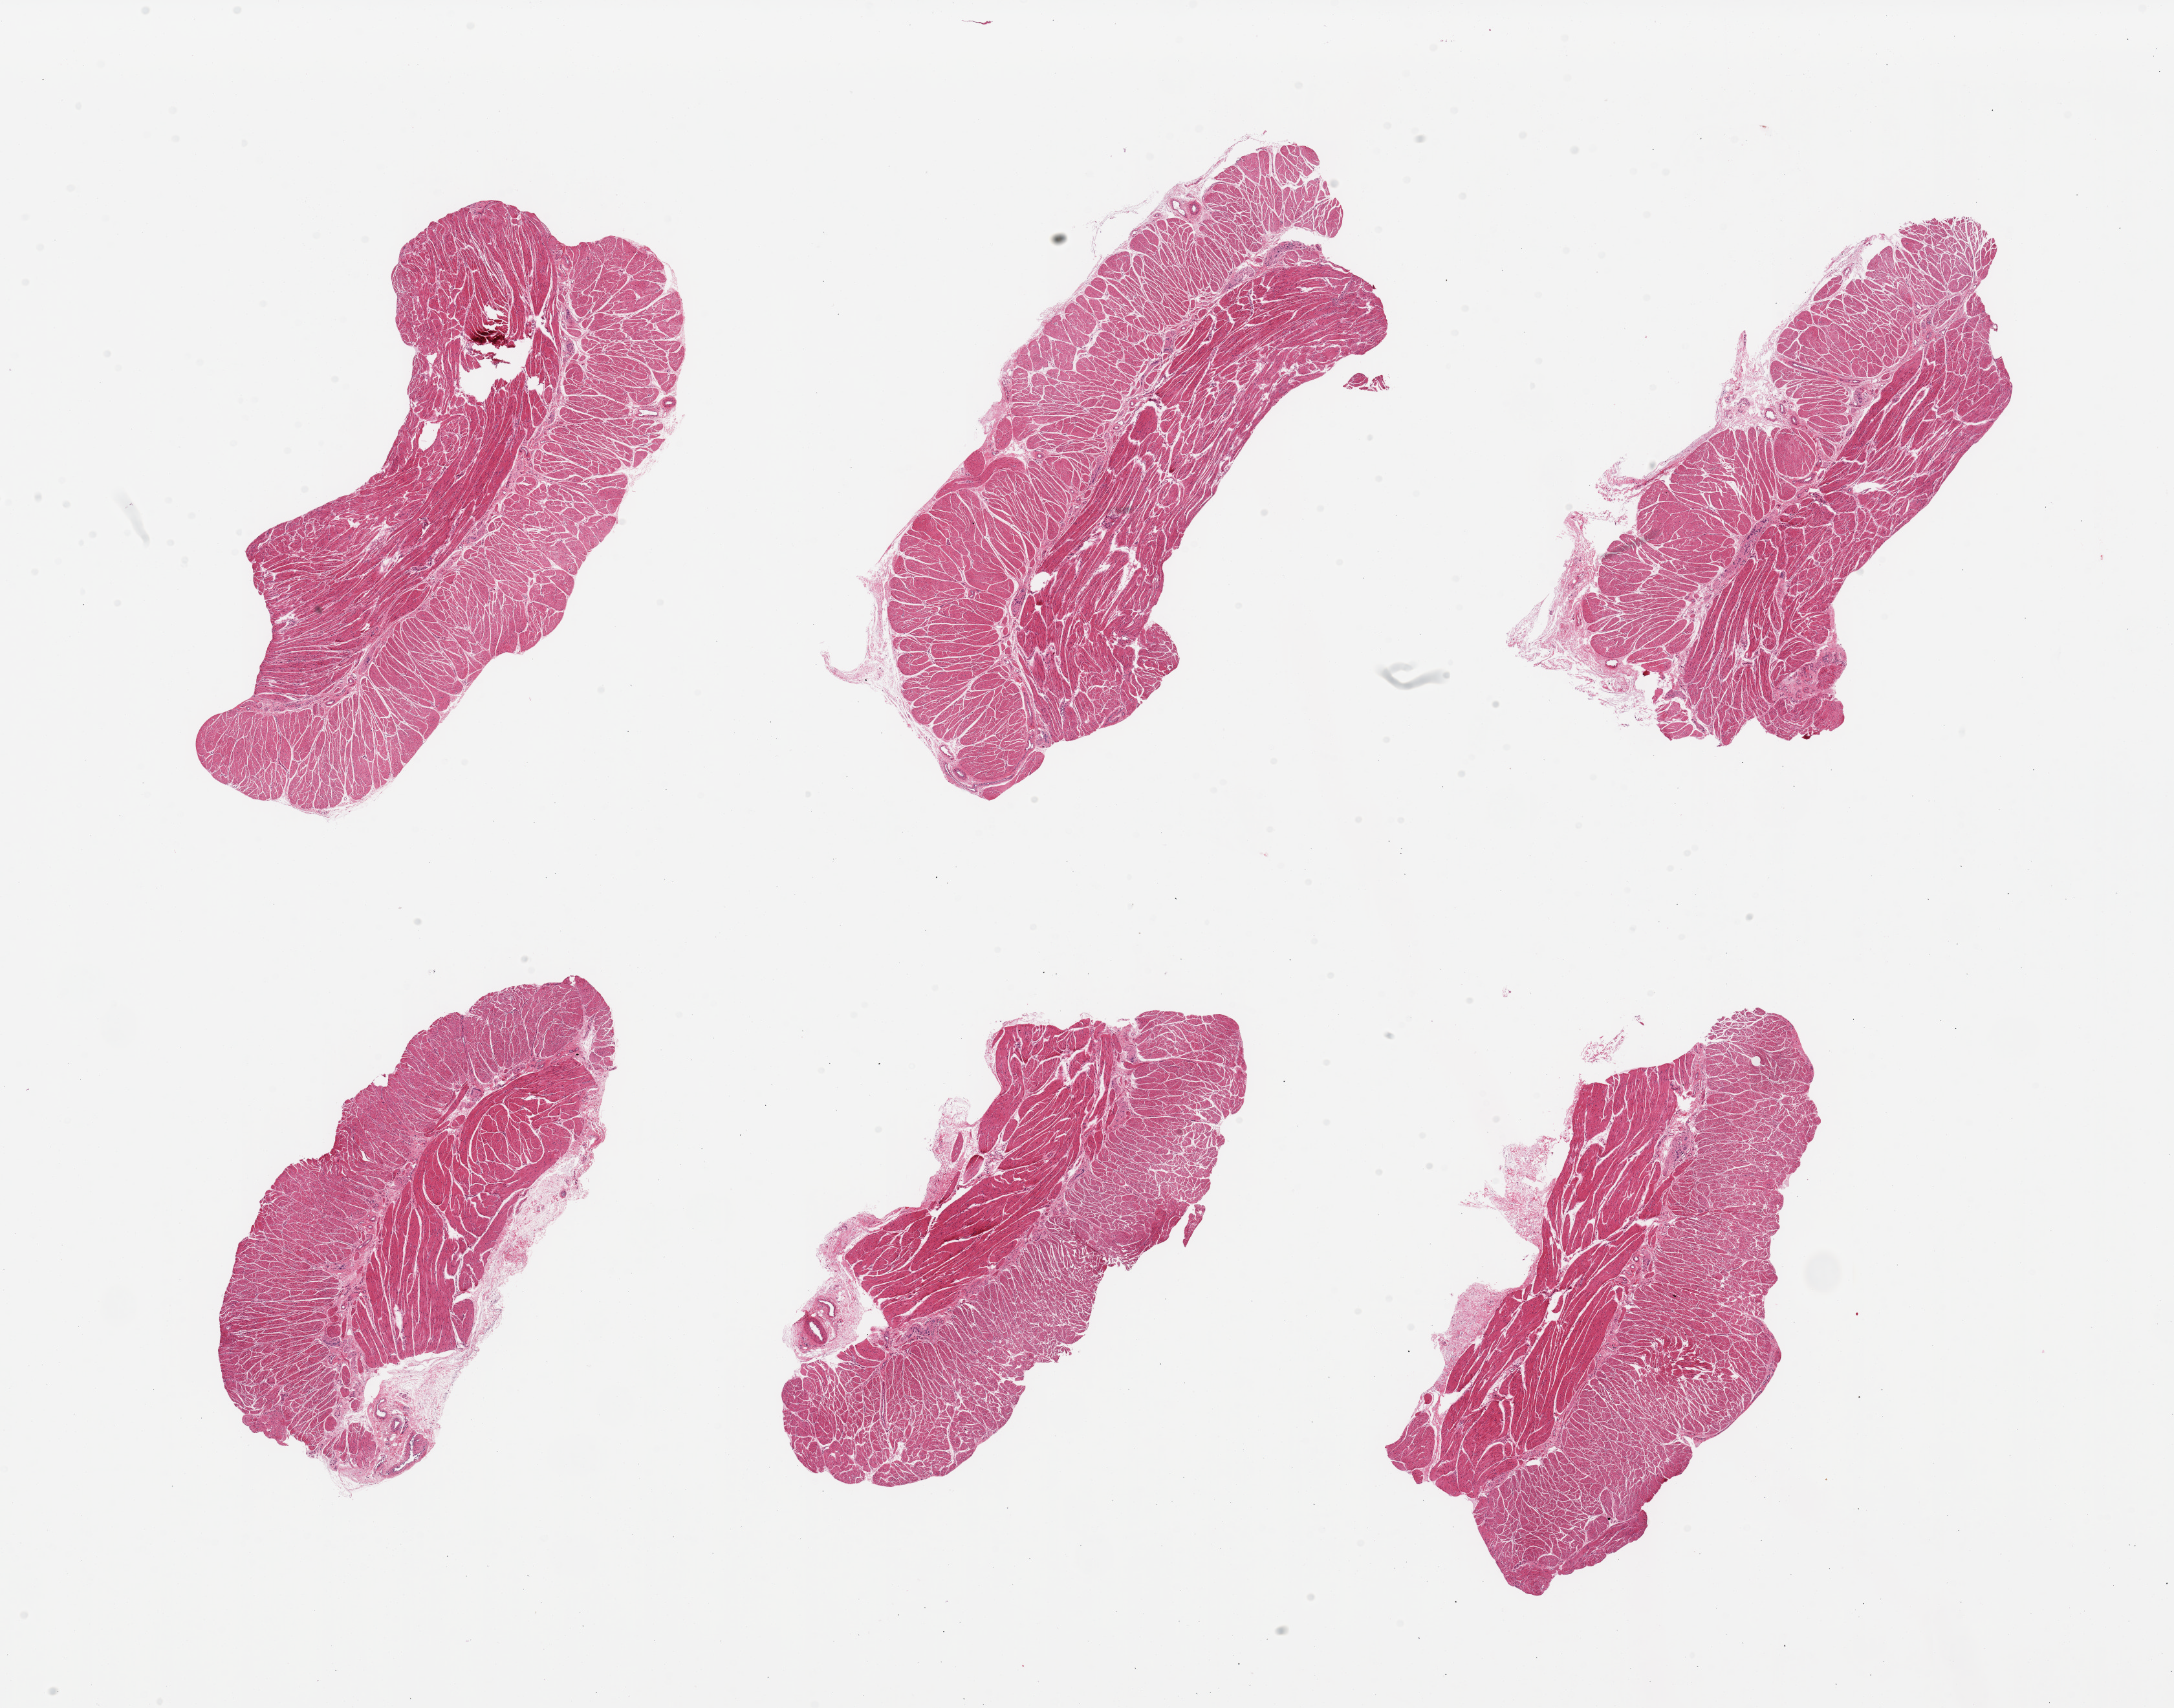
Whole-slide image, hematoxylin and eosin (H&E) stain, brightfield — low-resolution overview of the scanned area, about 26.6 x 20.9 mm. PAXgene-fixed paraffin-embedded (PFPE) section. Section of gastroesophageal junction (target tissue). Tissue donor sample. Donor sex: male.
Reviewer comment on this tissue sample: 6 pieces; target muscularis.